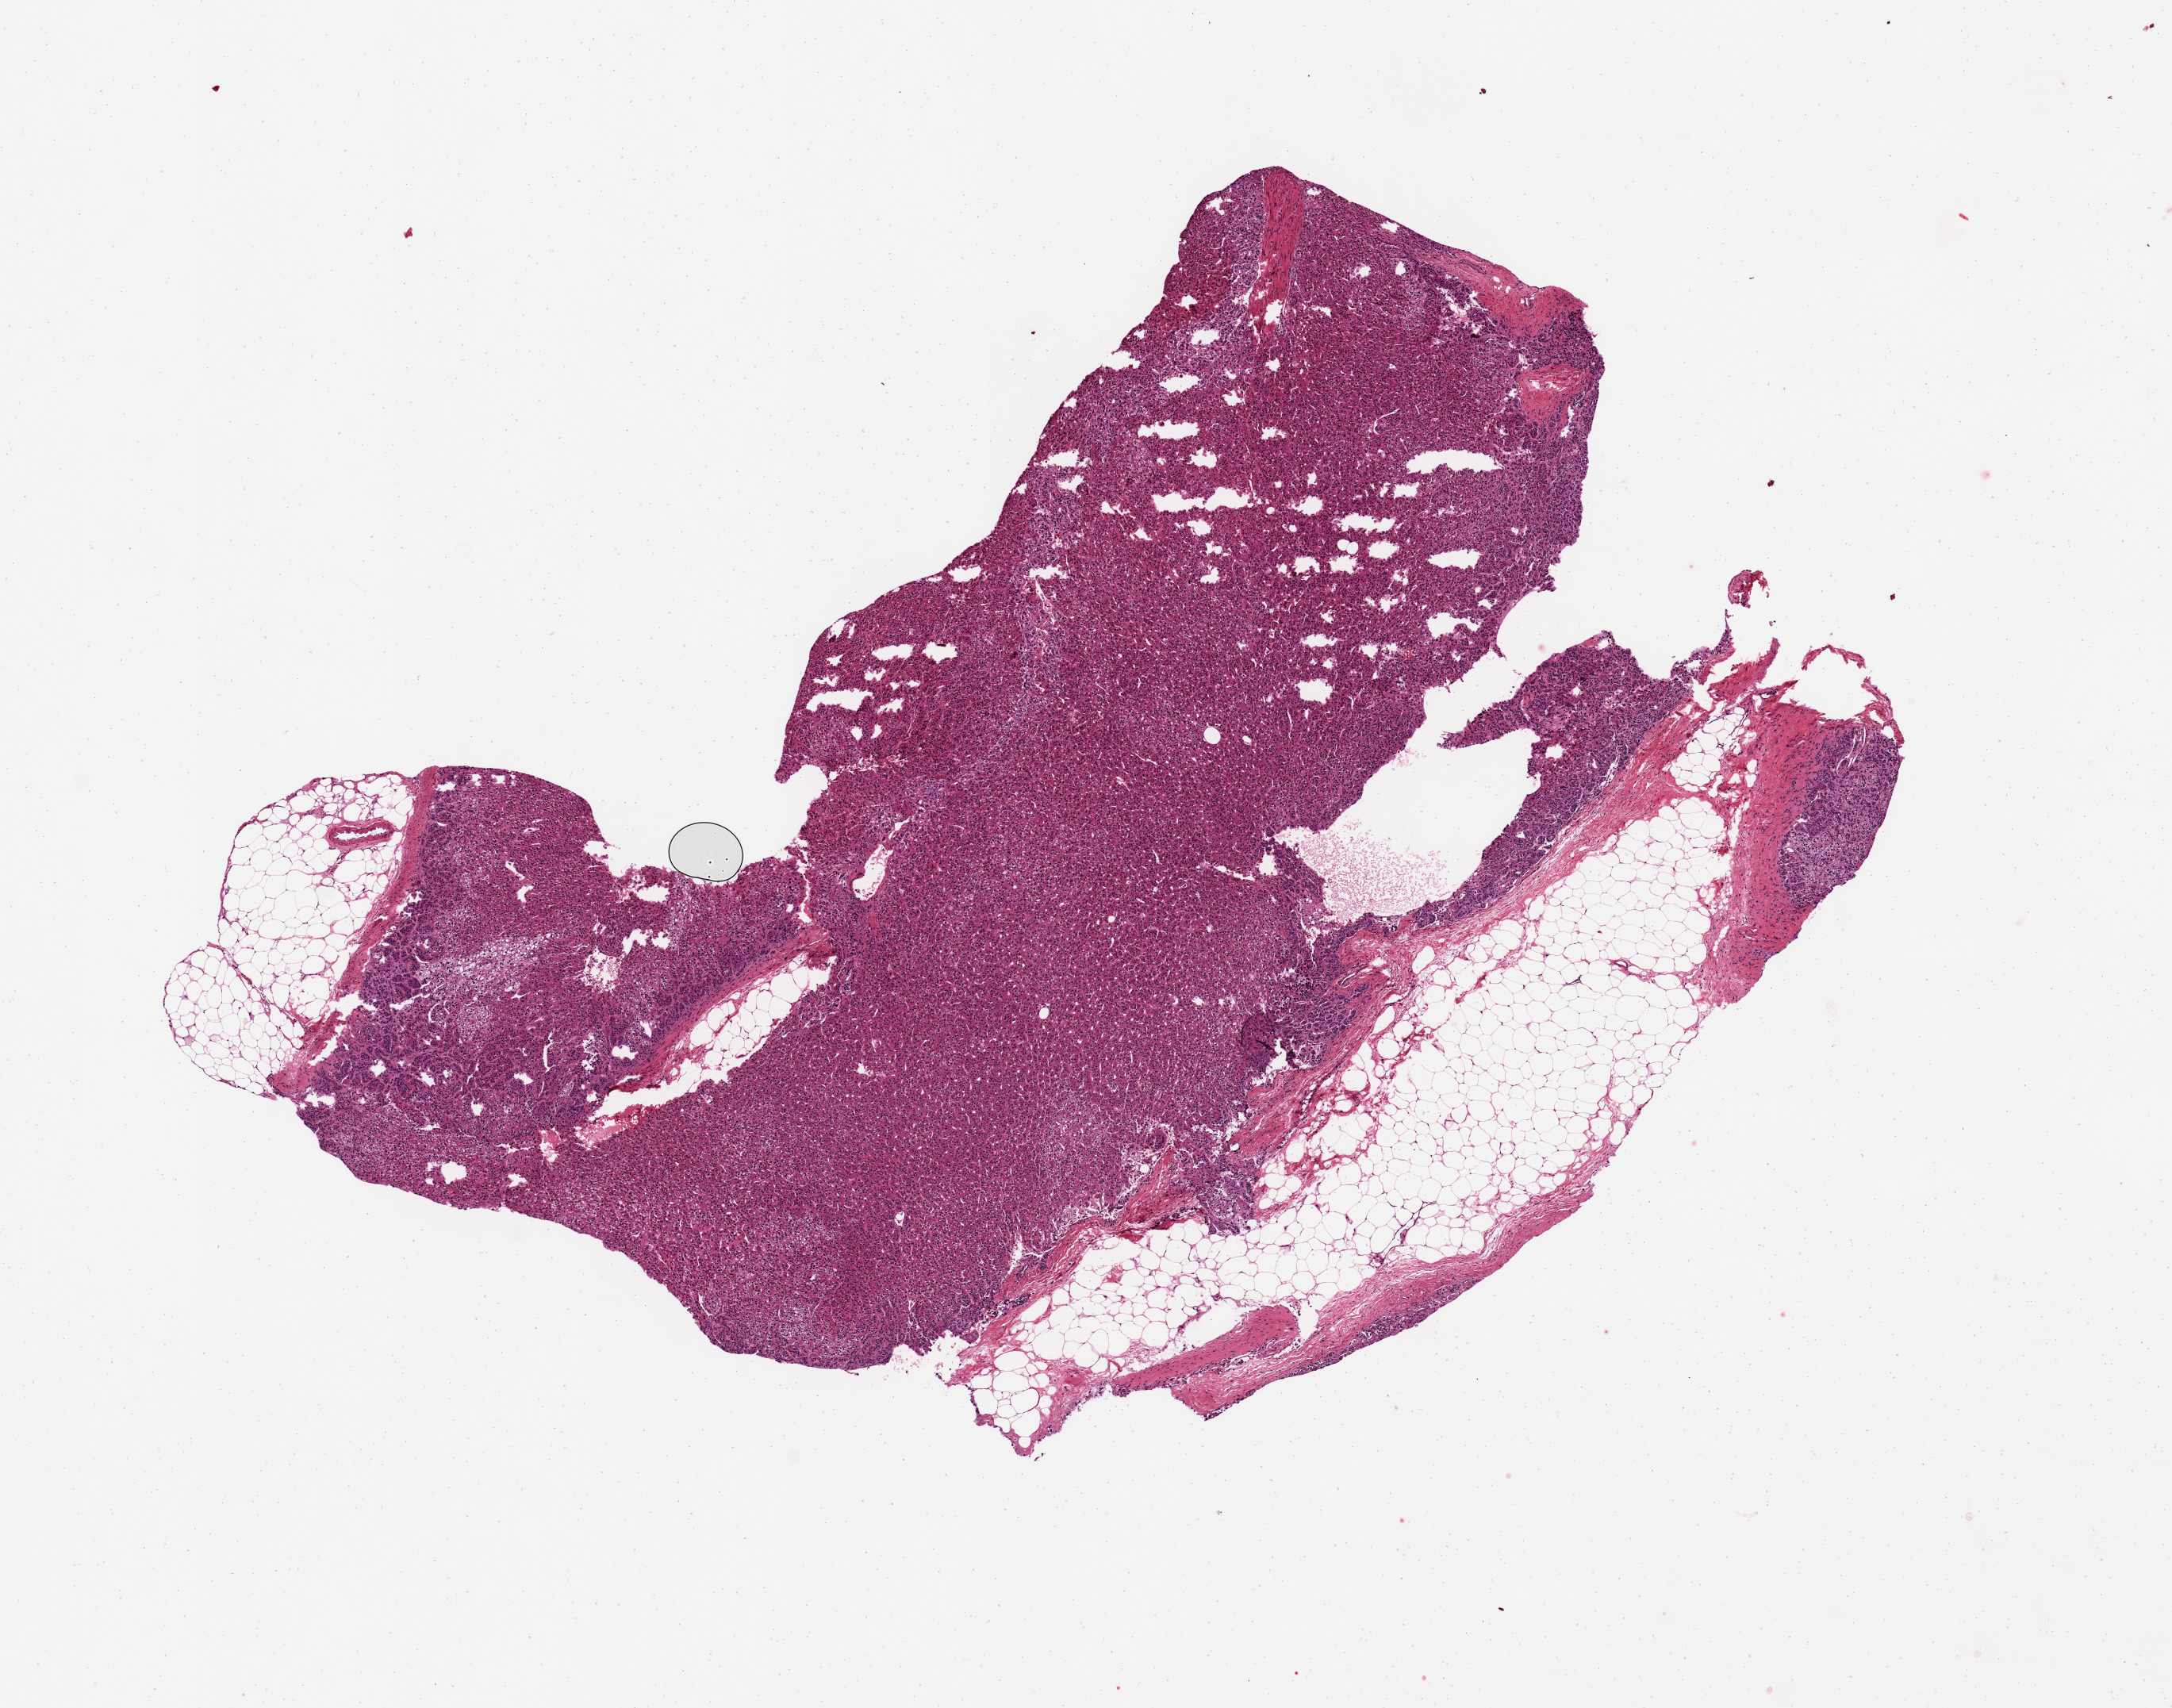
H&E whole-slide image, shown as a low-resolution overview of the whole scanned area (about 10.8 x 8.5 mm). PAXgene-fixed paraffin-embedded (PFPE) section. Sampled site (target tissue): adrenal gland. Tissue donor sample. Male donor.
Reviewer comment on this tissue sample: 40% adipose . 7x6.5mm.